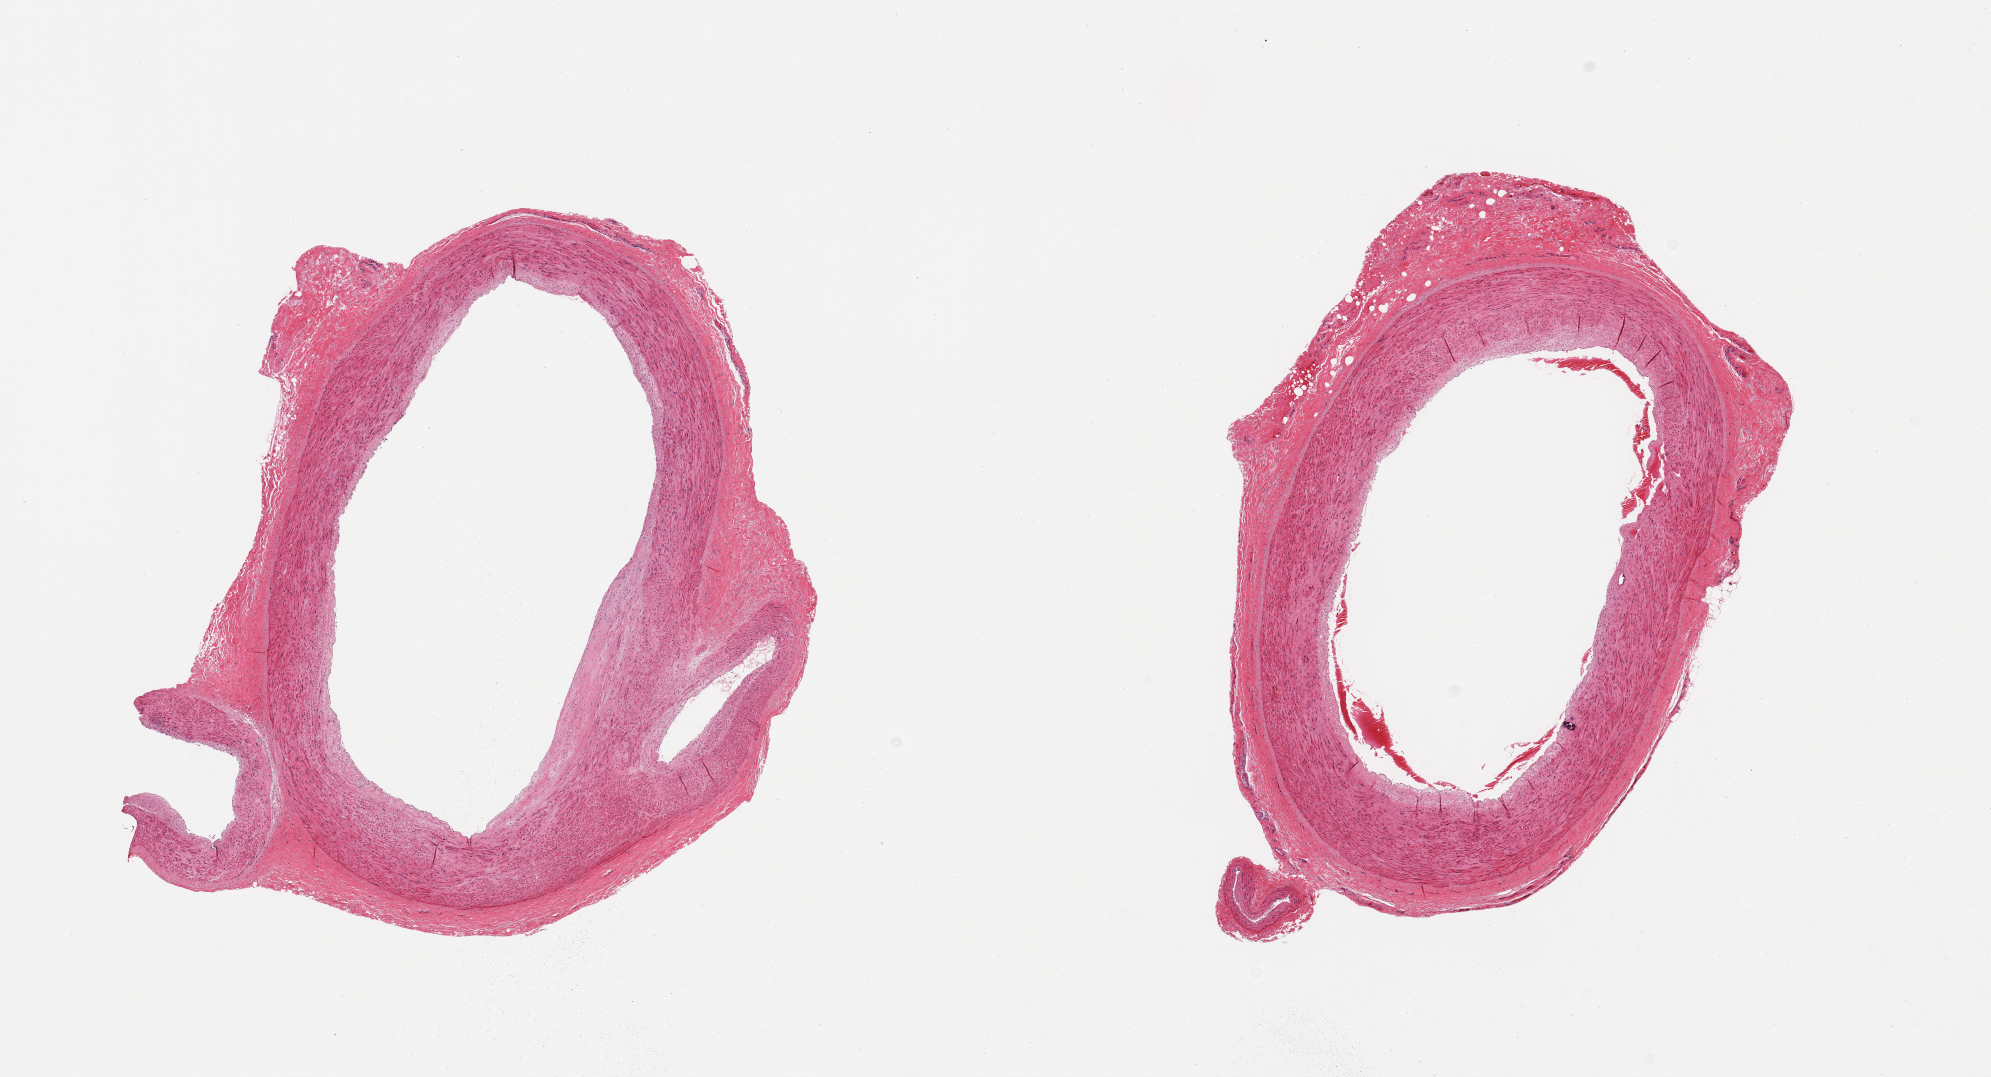
Whole-slide image, haematoxylin and eosin stain, shown as a low-resolution overview of the whole scanned area (about 15.8 x 8.5 mm, from a 20x scan); PAXgene-fixed, paraffin-embedded tissue; sampled site (target tissue): tibial artery; tissue donor sample.
* review note (as recorded): 2 pieces; early plaque formation; focal calcification; attached adventitia with accessory vessels